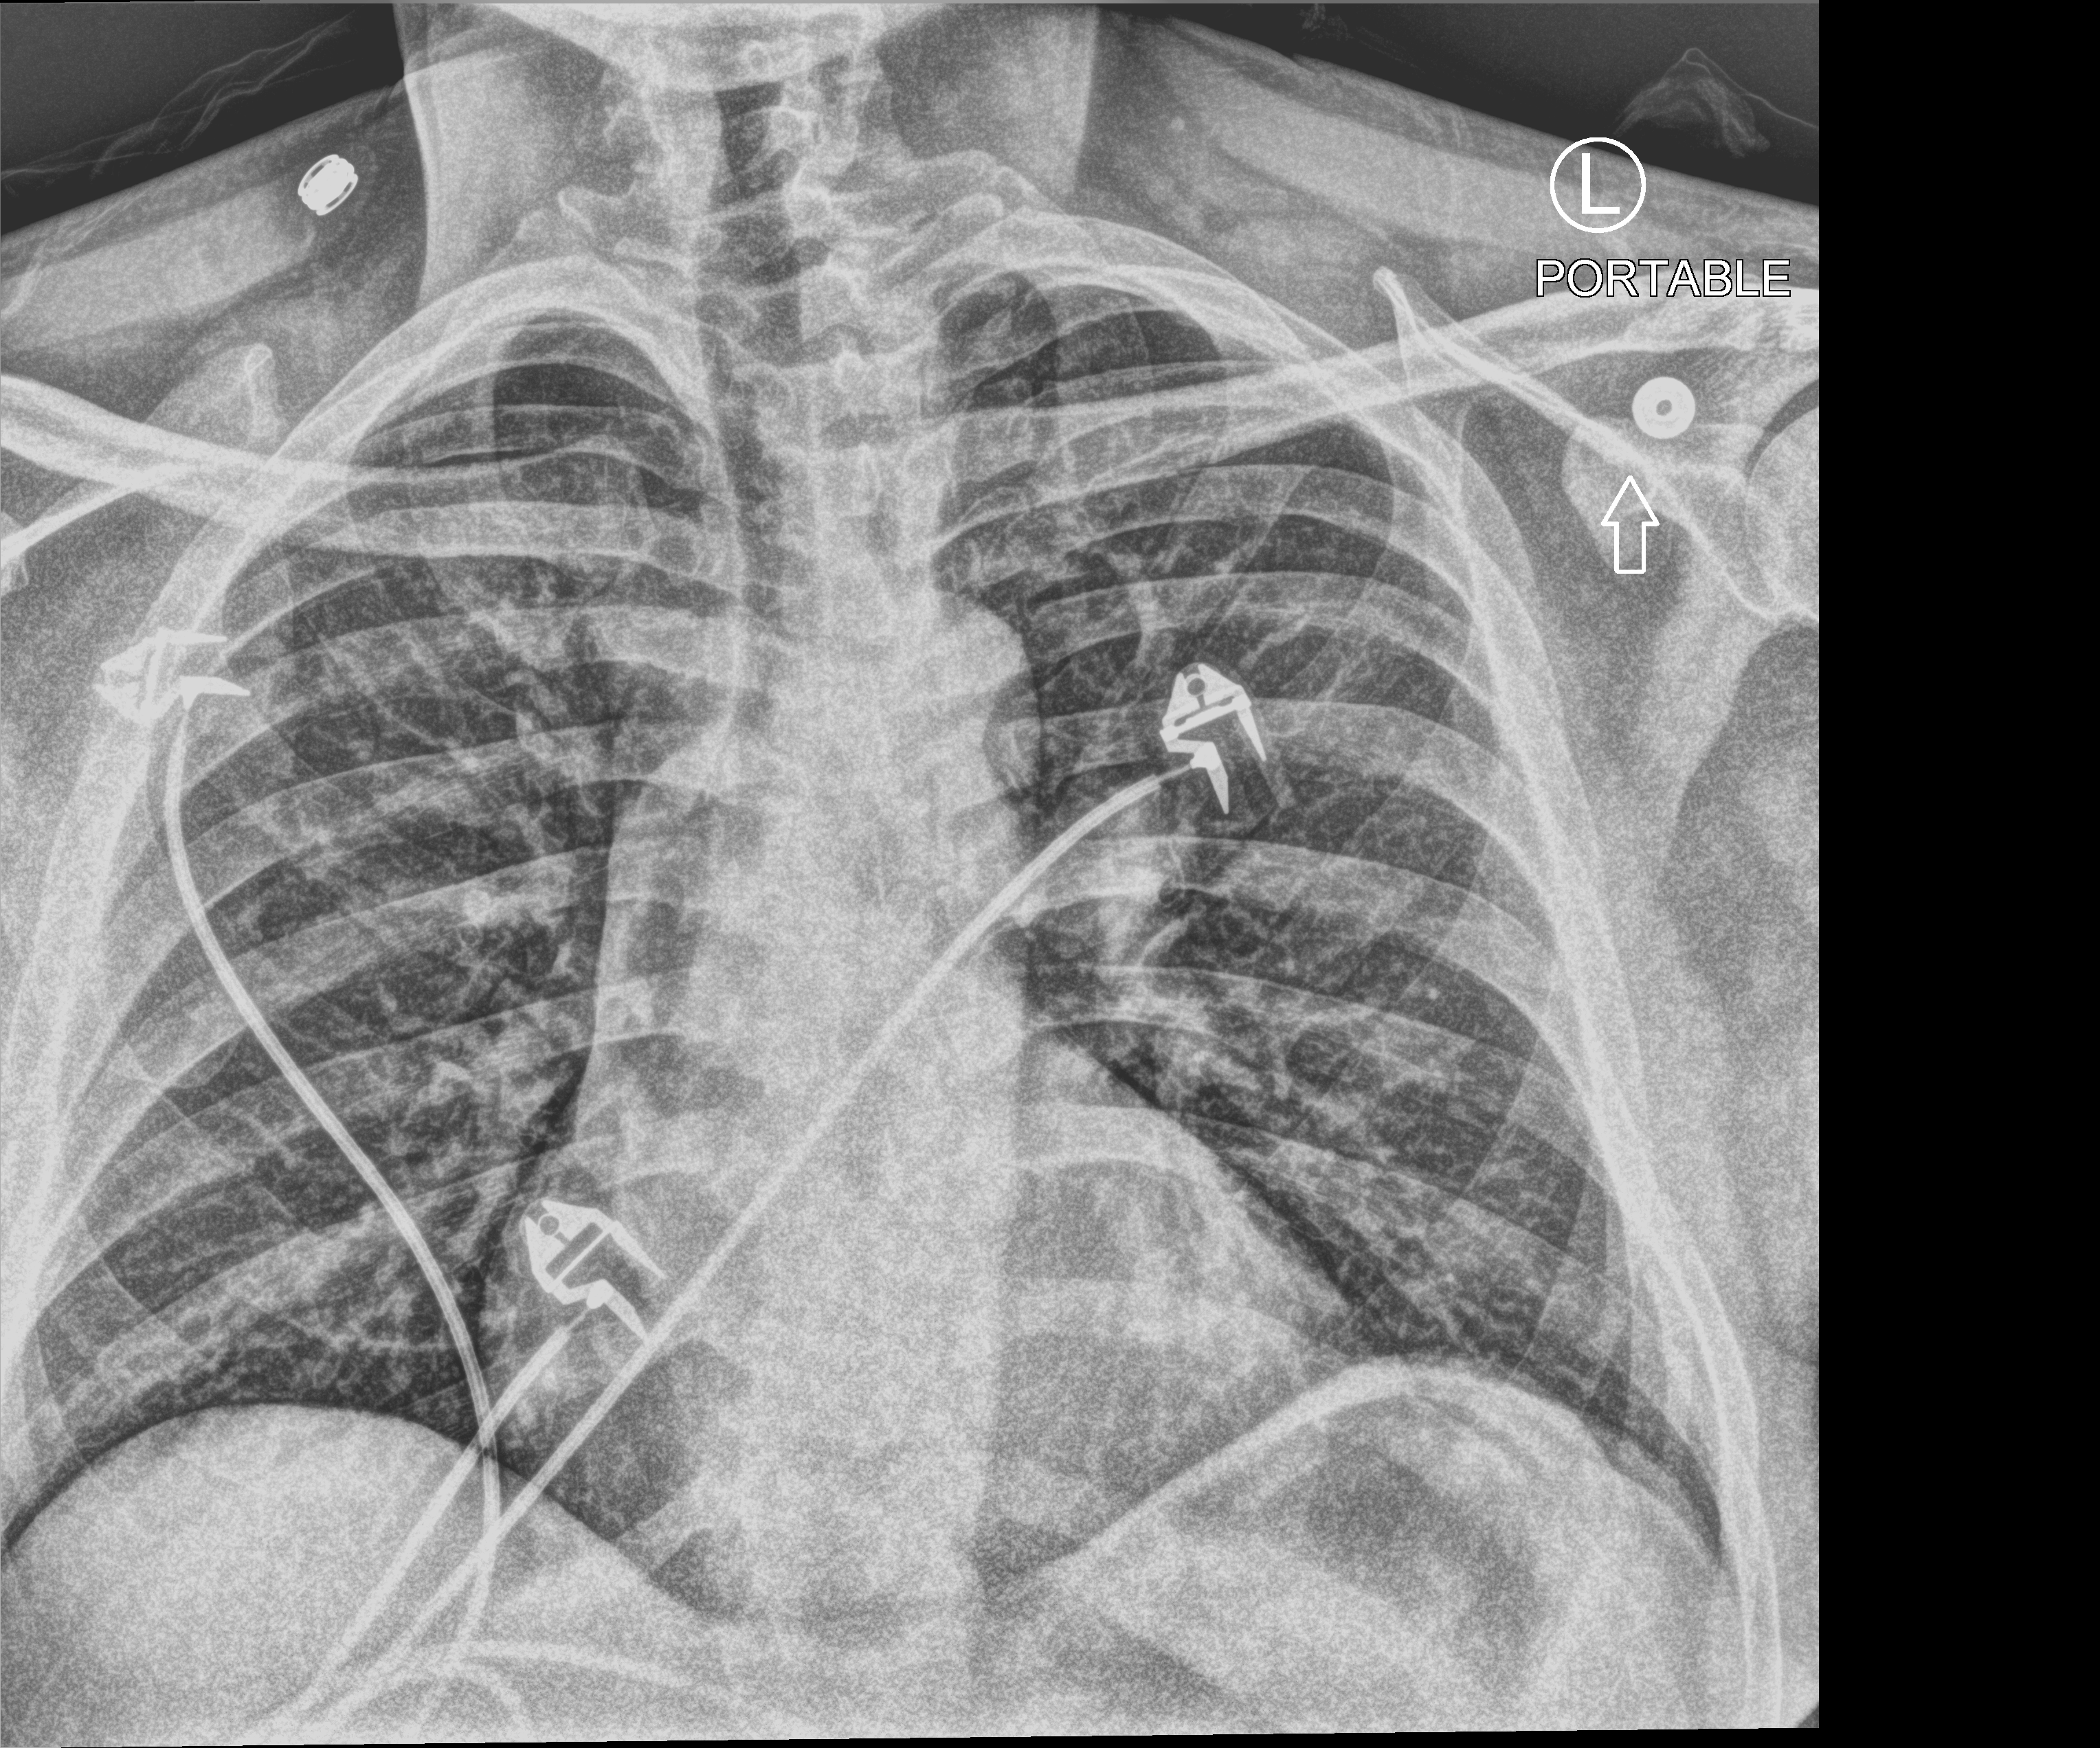
Portable chest radiograph; anteroposterior (AP) projection. Patient hospitalised with COVID-19; male, aged 18–59 years.
Hospital-stay facts (about this admission, not read from this image; timing relative to this image not recorded): admitted to intensive care during this hospital stay: no; mechanically ventilated during this hospital stay: no; COPD (admission record): no.